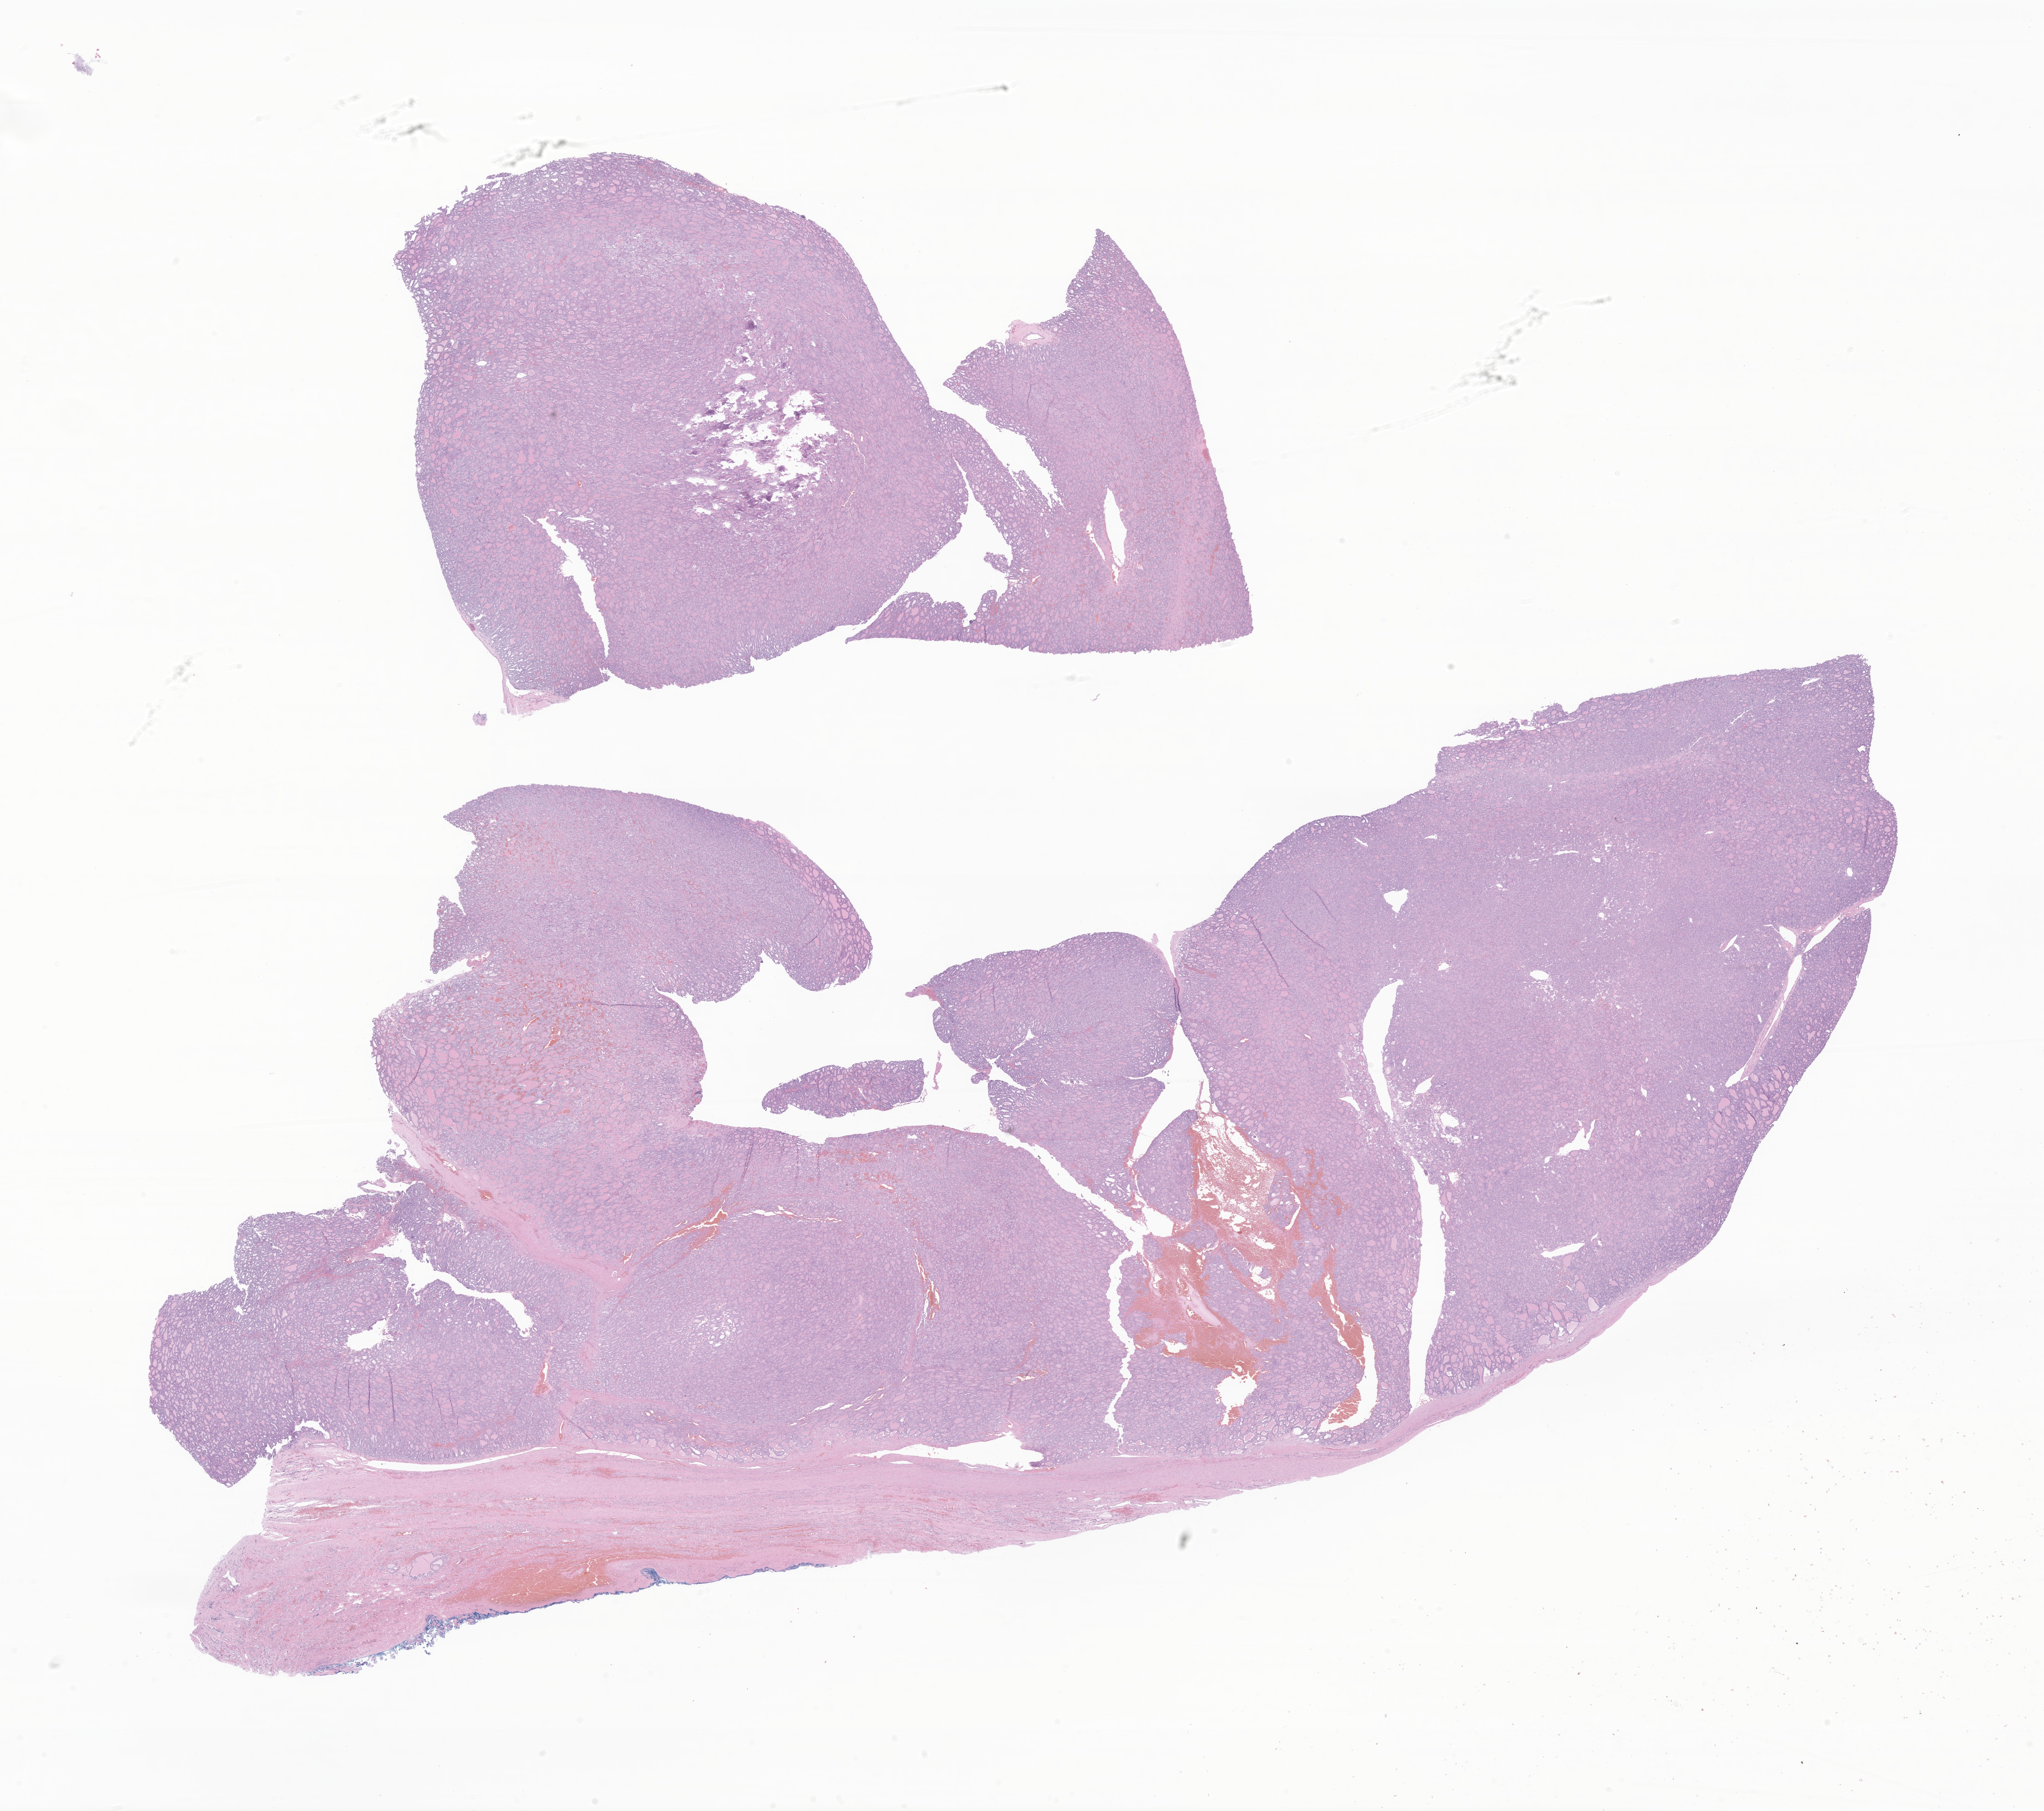
Whole-slide image, H&E stain of tumor tissue from the thyroid — whole scanned area (about 25.5 x 22.6 mm) shown as a low-resolution overview; formalin-fixed, paraffin-embedded (FFPE) tissue. Female patient, age 176 months.
Diagnosis (ICD-O-3 morphology term): Papillary carcinoma, NOS.